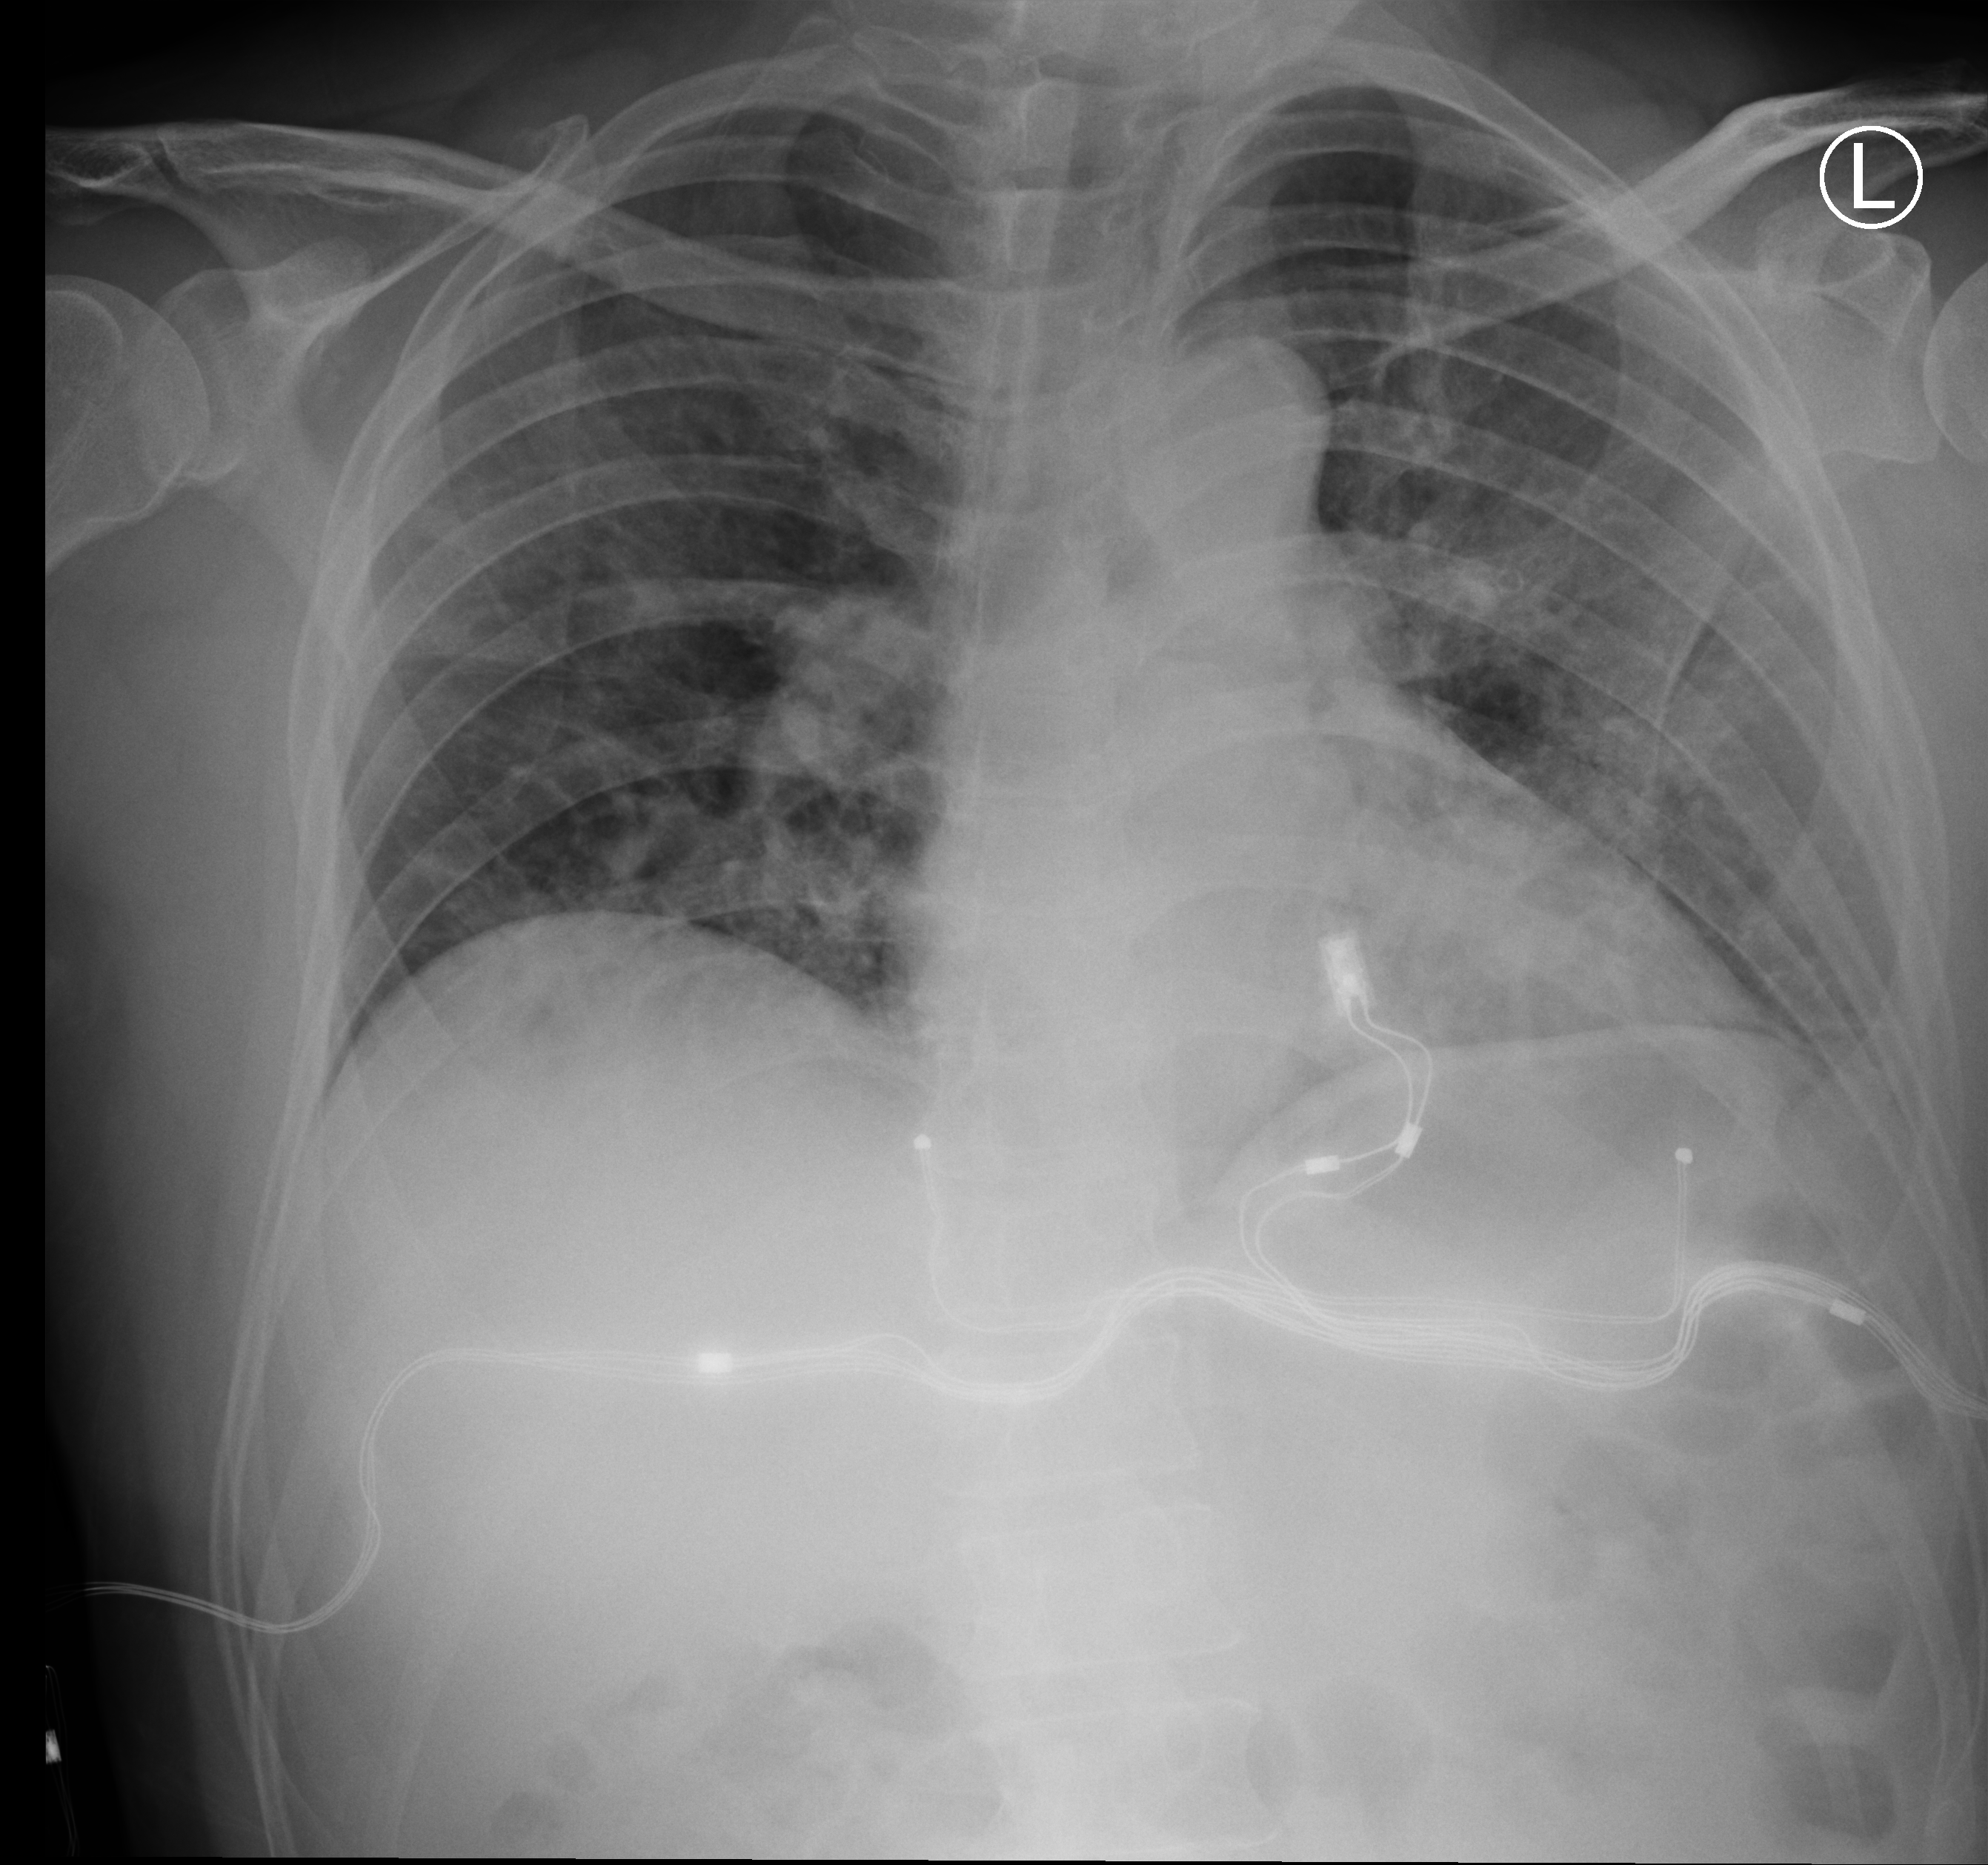
Chest X-ray (portable); anteroposterior (AP) projection. Male patient hospitalised with COVID-19, age 18–59 years.
From the hospital-stay record, not from the radiograph (when in the stay this image was taken is not recorded):
- mechanically ventilated during this hospital stay: no
- smoking status (admission record): never